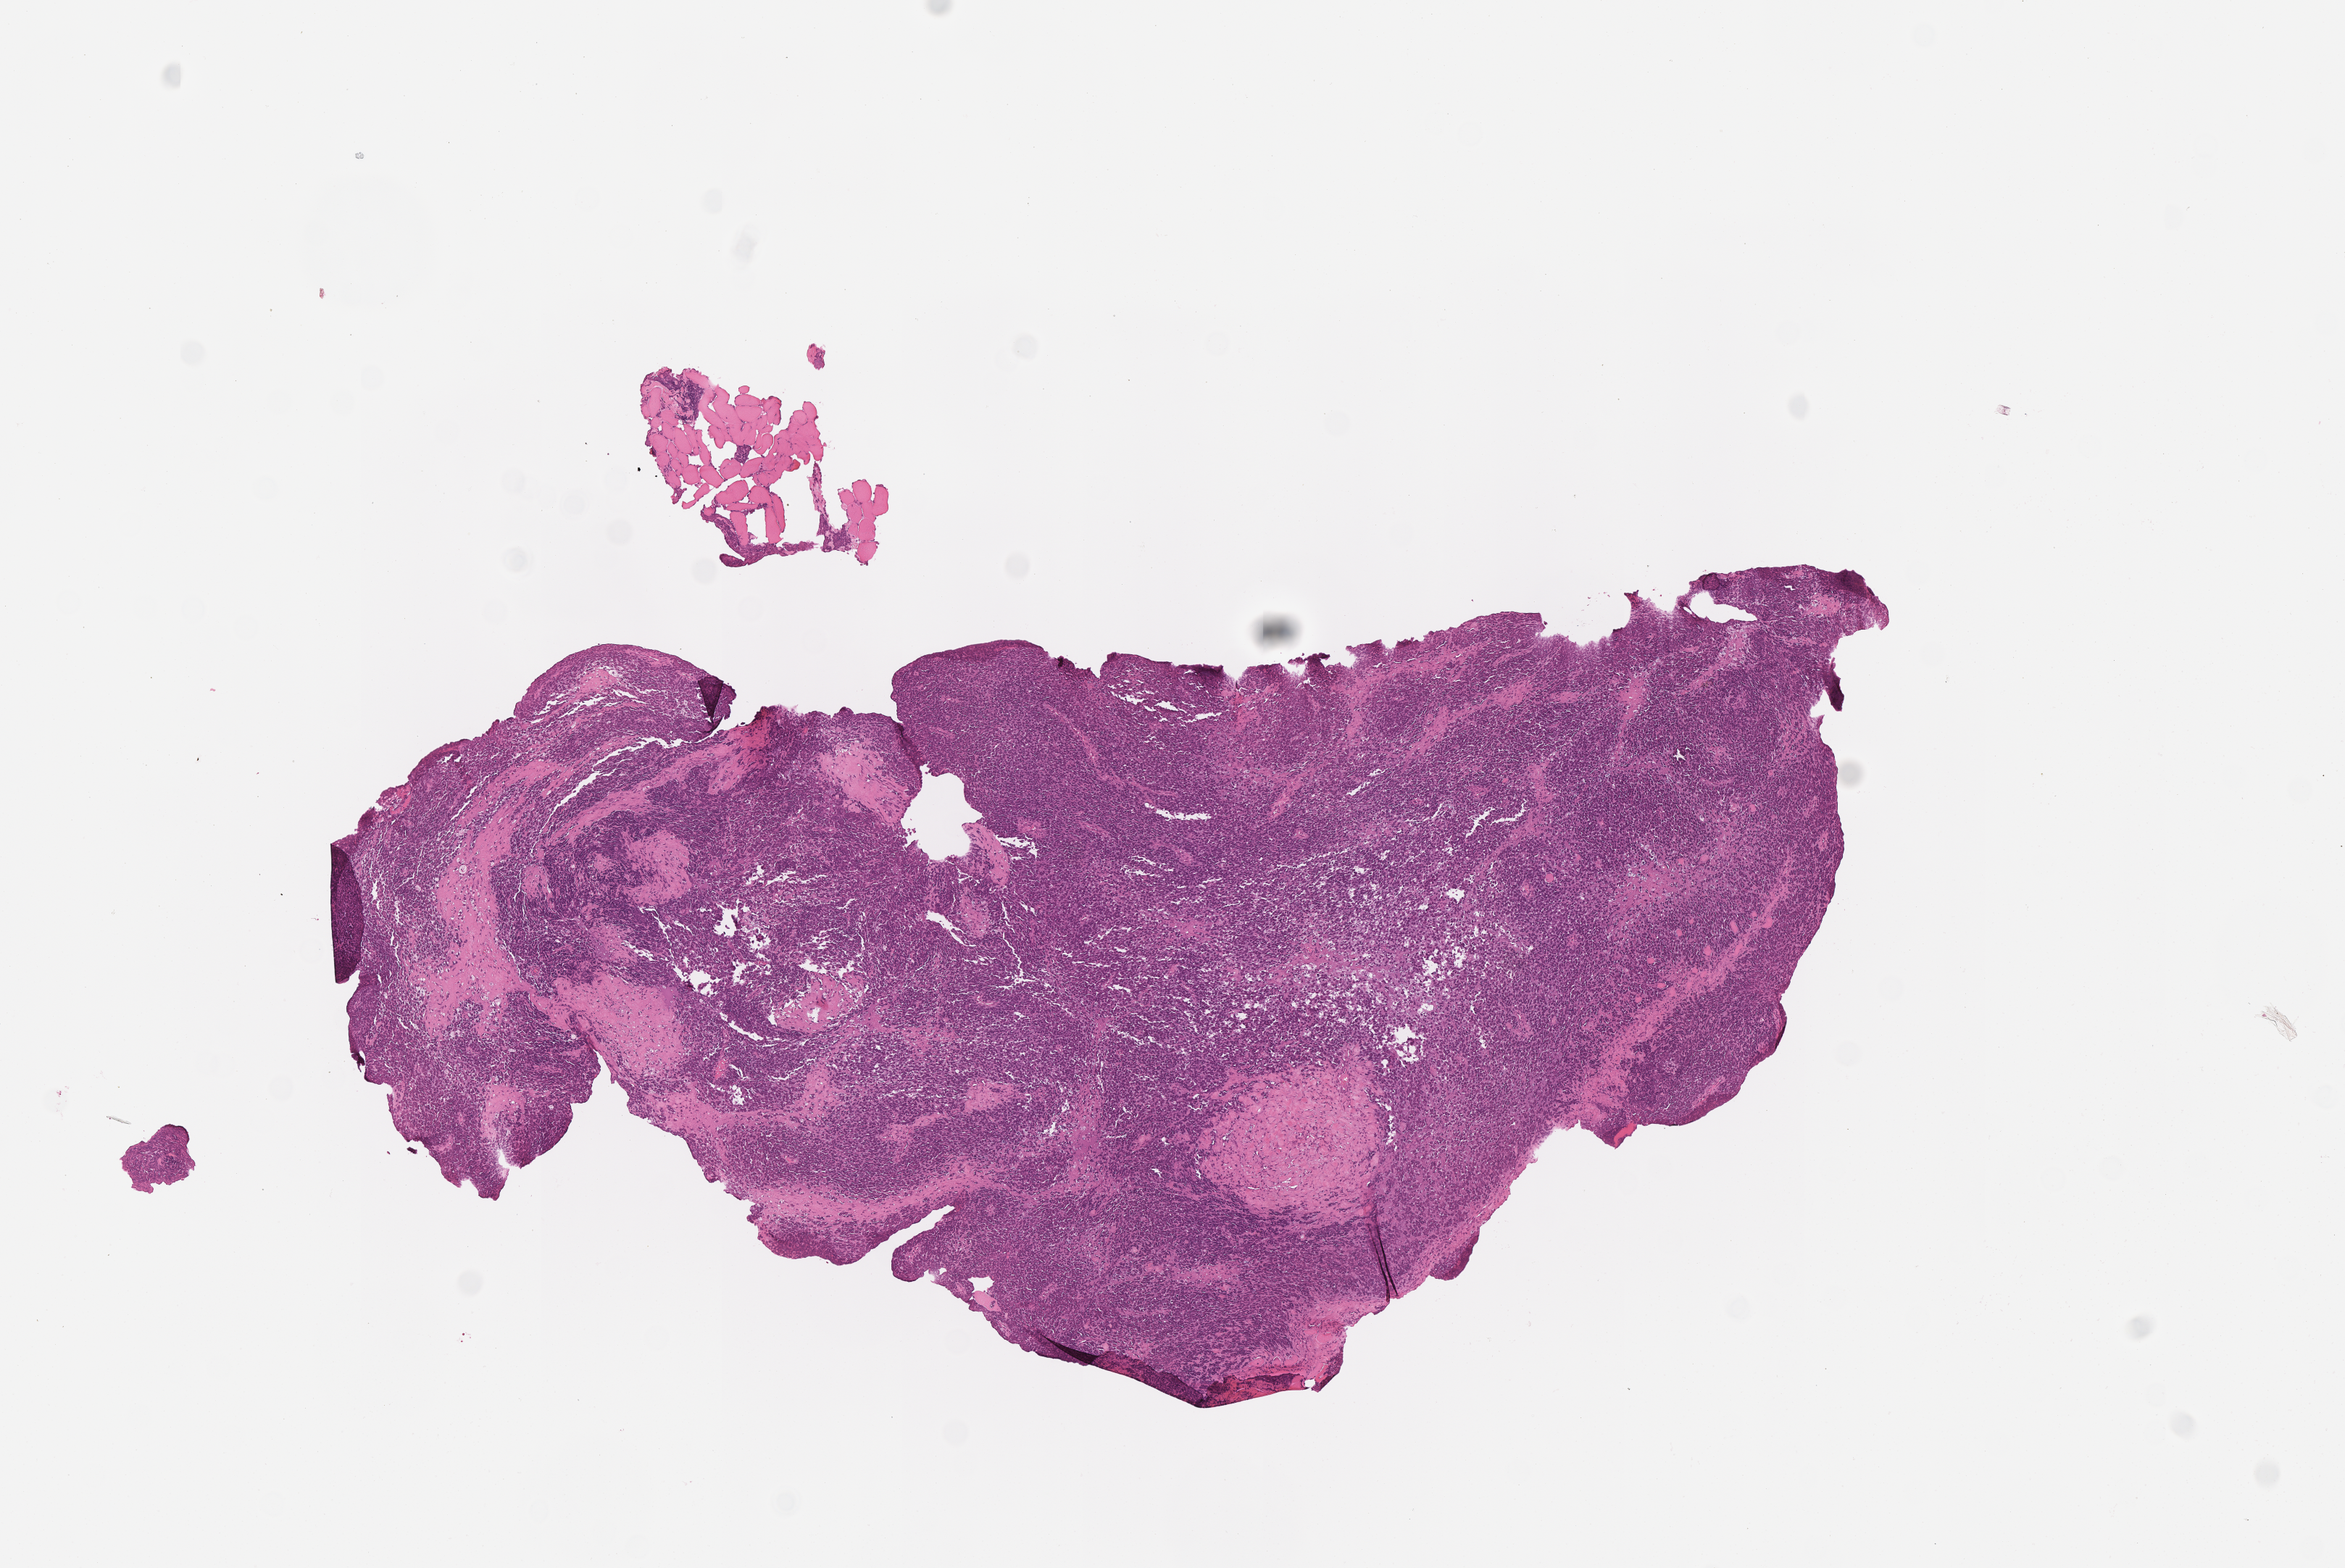
Whole-slide image, haematoxylin and eosin stain of tumor tissue, whole scanned area (about 6.5 x 4.4 mm) shown as a low-resolution overview. Formalin-fixed, paraffin-embedded (FFPE) tissue. Site: elbow, right. Female patient, age at diagnosis 14.7 years.
Metastatic status at presentation (as recorded): metastatic (confirmed). Diagnosis: rhabdomyosarcoma; histological classification: alveolar rhabdomyosarcoma. Stage (as recorded): 4.